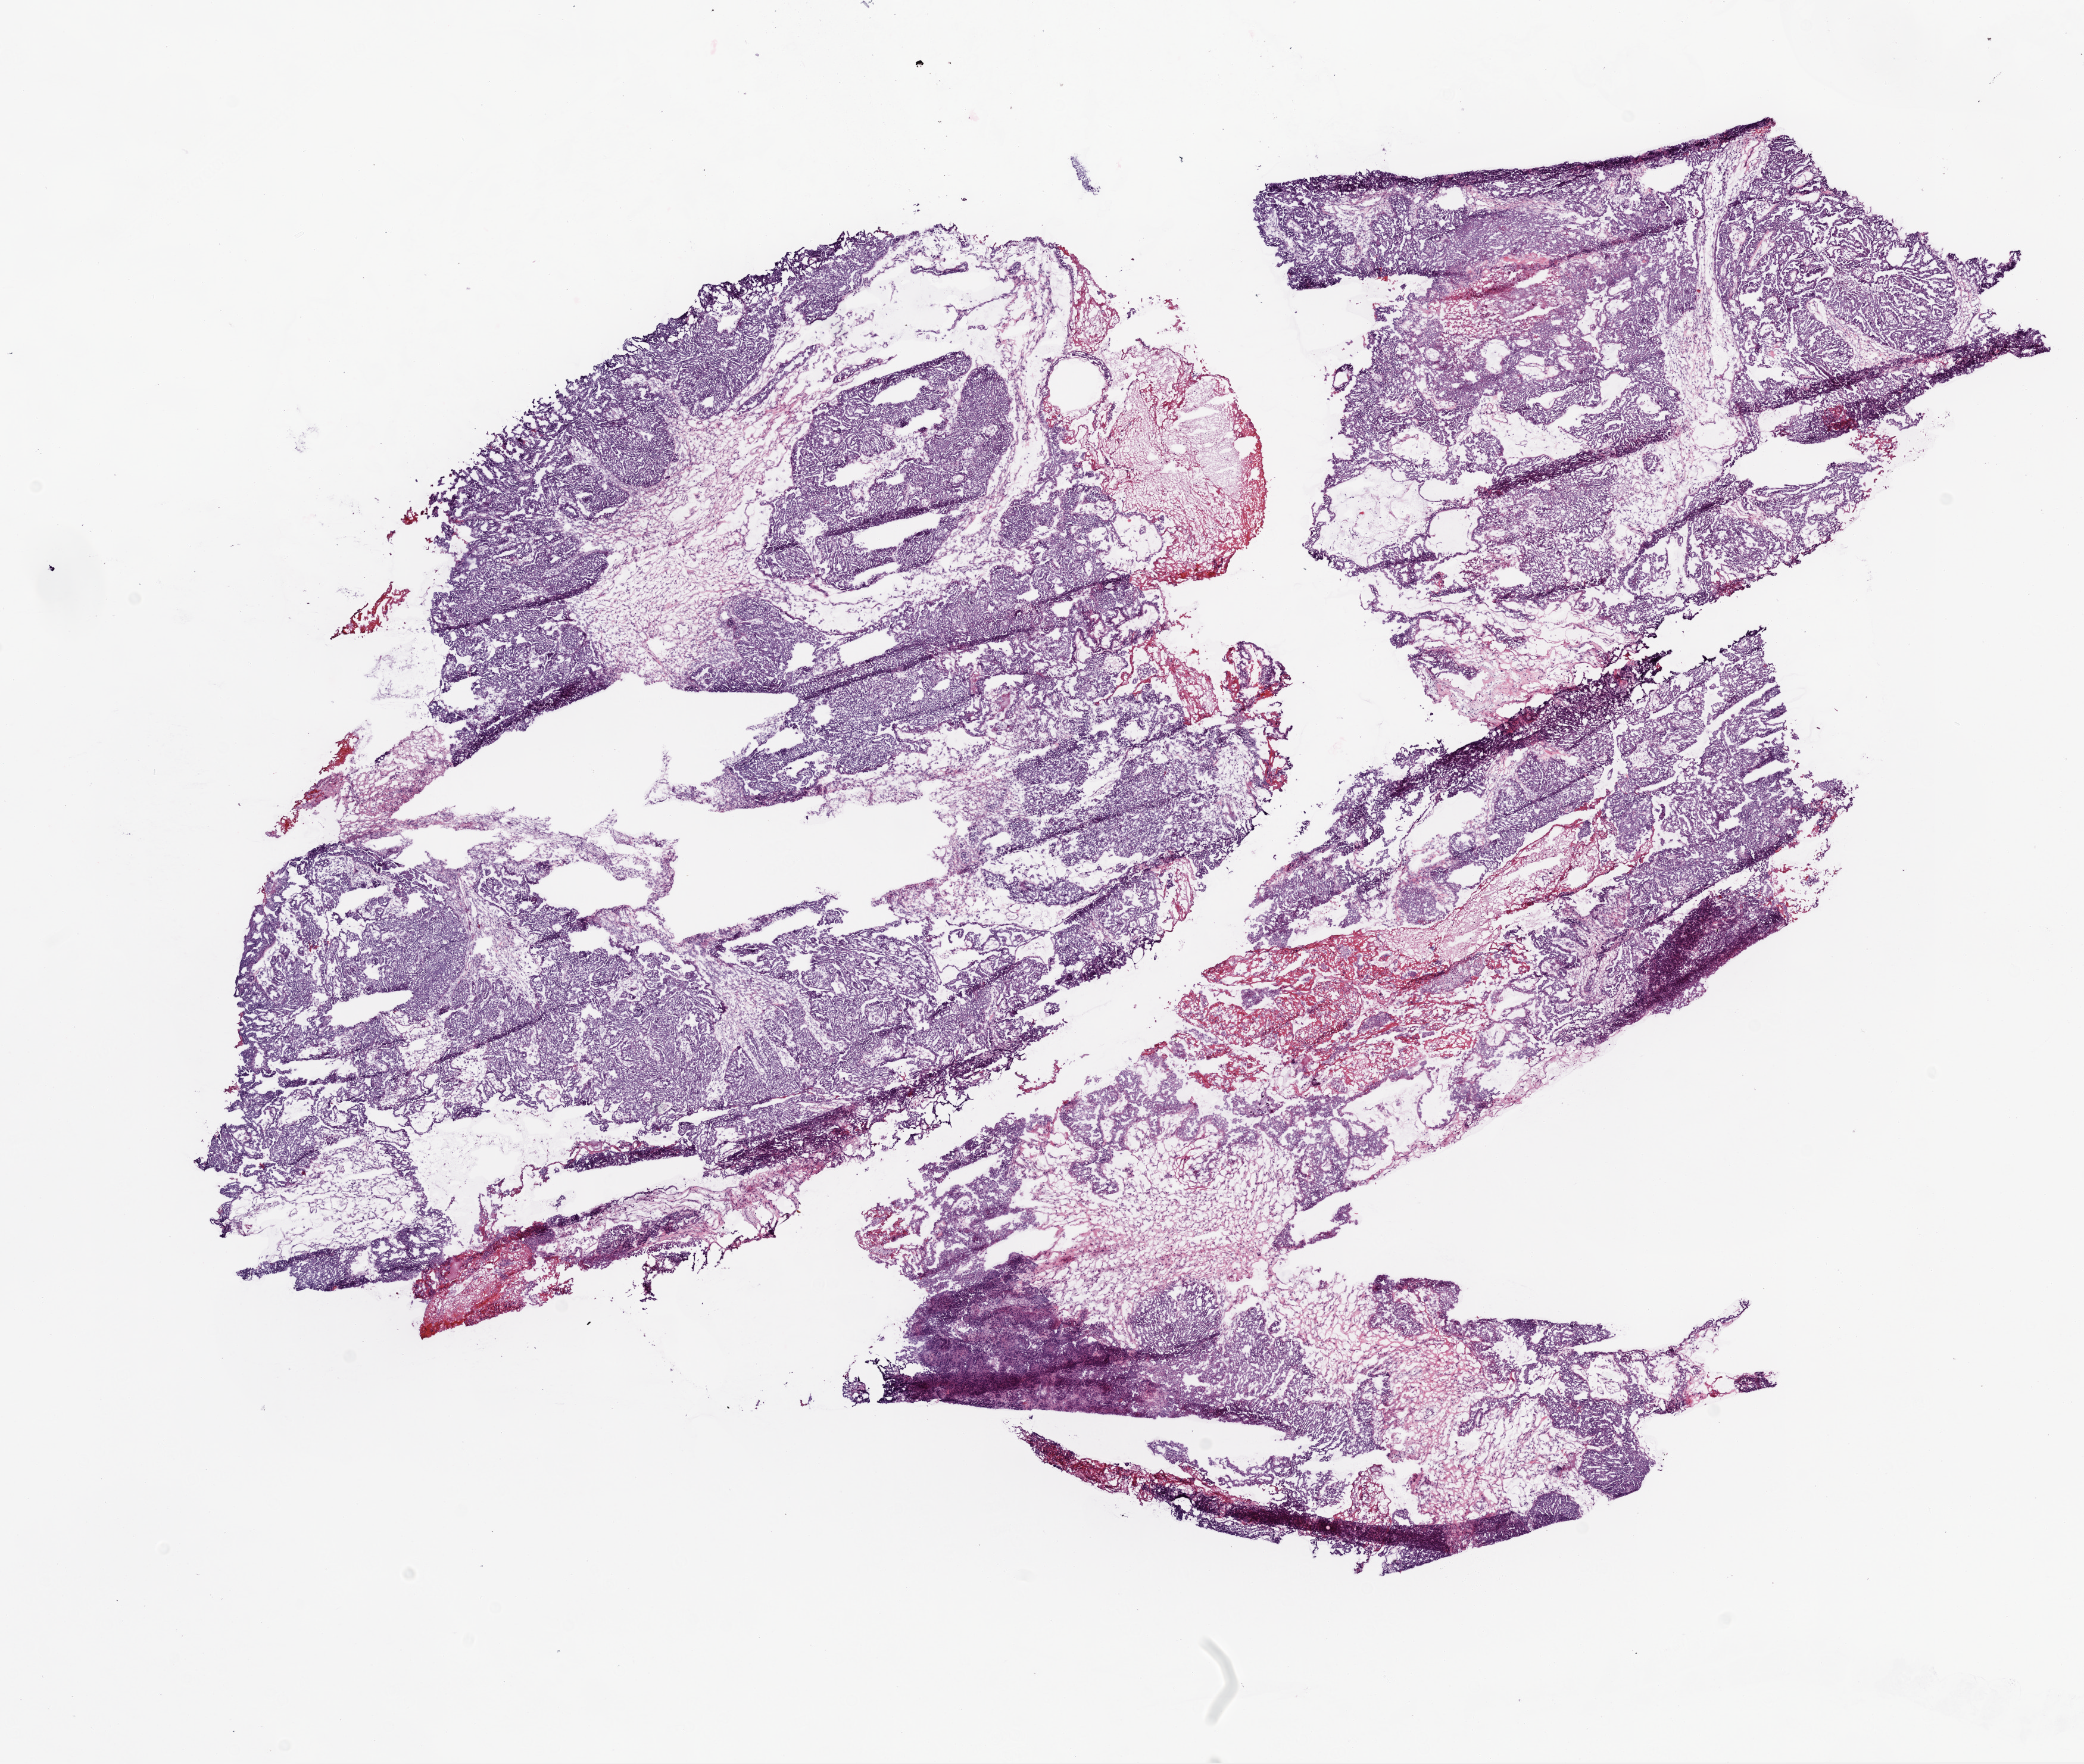
Whole-slide histology image, Hematoxylin and eosin (H&E) stained, low-resolution overview of the scanned area, about 14.0 x 11.9 mm (acquisition: 20x scan). Frozen section from the top of the tissue portion. Primary tumour sample from the ovary. Patient: female, age at initial diagnosis 58 years. Histologic grade: G3 (poorly differentiated). Composition of this section per pathologist review: tumour cells 94%, tumour nuclei 95%, normal cells 0%, stromal cells 5%, necrosis 1%.
* FIGO stage: IV
* histologic diagnosis: Serous cystadenocarcinoma, NOS